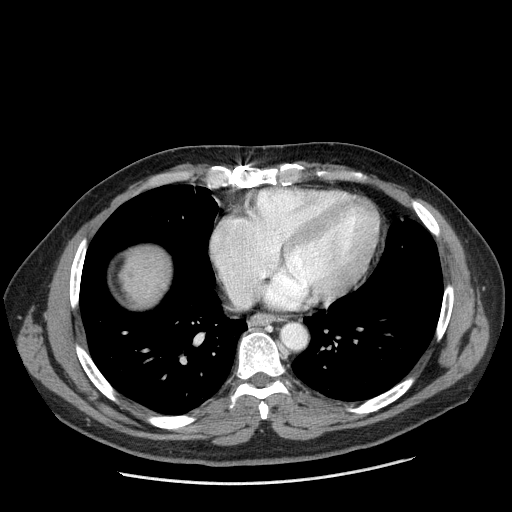
Contrast-enhanced abdominal CT (liver protocol), one axial slice. Position 185 of 198 along the scan axis. Reconstruction kernel STANDARD. 120 kVp. One of 2 acquisitions stored at this slice position. Soft-tissue window (W 400 / L 40 HU). 512 × 512 image matrix, field of view 400 × 400 mm. From the clinical record (not read from this slice): diagnosis: hepatocellular carcinoma (patient treated with transarterial chemoembolisation; whether this scan precedes or follows treatment is not stated here); TNM stage (as recorded): Stage-II; Child-Pugh class: A; tumour differentiation: moderately differentiated; tumour nodularity: multinodular.
Structures marked on this image (semi-automatically segmented with operator editing):
- liver parenchyma outside the tumour (the mass and vessels are separate outlines, so this box may not span the whole liver): bounding box [x1, y1, x2, y2] px = [120, 245, 170, 306]